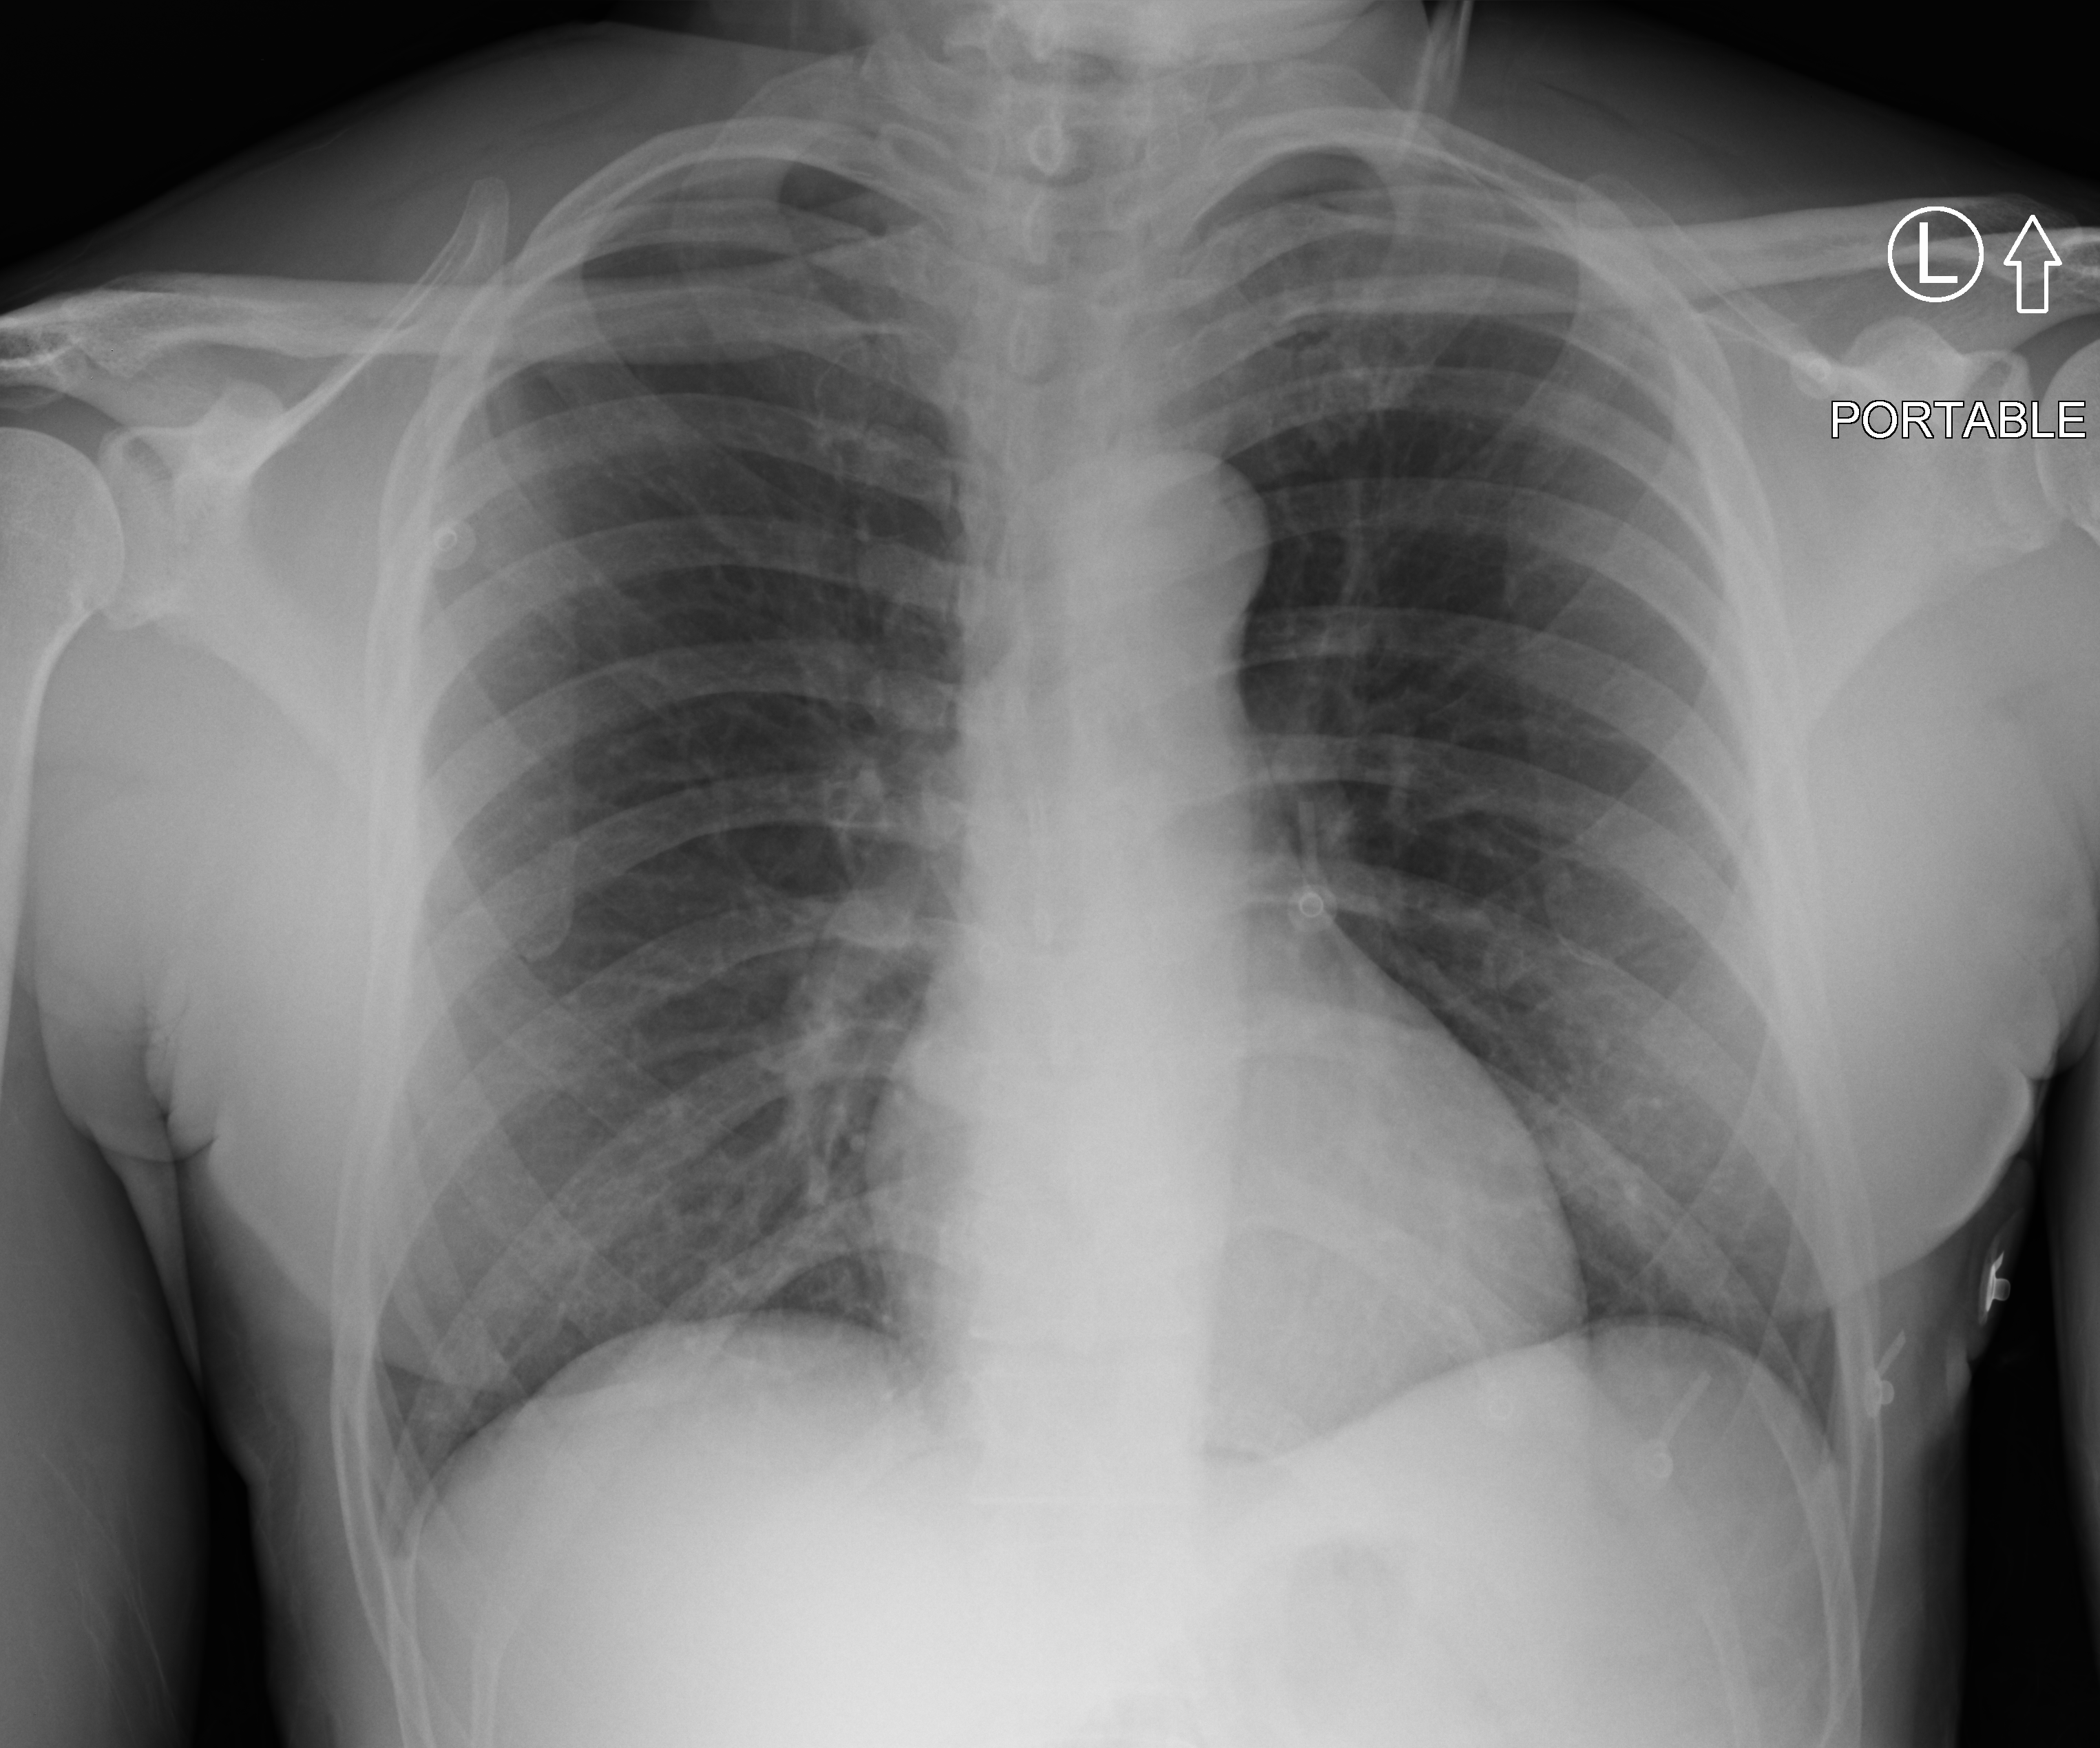
Chest X-ray (portable), anteroposterior (AP) projection. Patient hospitalised with COVID-19; male, aged 18–59 years.
Hospital-stay facts (about this admission, not read from this image; timing relative to this image not recorded): mechanically ventilated during this hospital stay: no; length of hospital stay: 11 days; admitted to intensive care during this hospital stay: no.